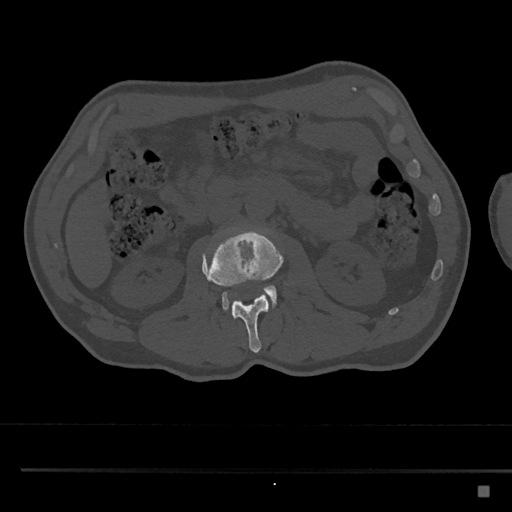
CT including the spine, one axial slice; position 740 of 797 along the scan axis; 120 kVp; bone window (W 1800 / L 400 HU); 0.5 mm slice thickness; 512 × 512 image matrix, field of view 391 × 391 mm. Patient: male, 59 years. Case-level facts recorded for this patient, not image findings: primary cancer: prostate.
Structures marked on this image (semi-automatically segmented with operator editing):
- L2 vertebra: bounding box (x1, y1, x2, y2) in pixels: (202, 228, 284, 353)
- L3 vertebra: (222, 285, 277, 312)